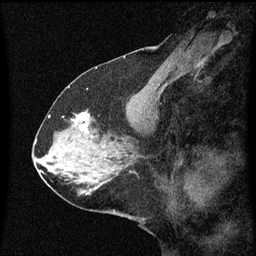
Breast MRI (dynamic contrast-enhanced), one sagittal slice. Slice 29 of 60 in the series (ordered by position). Dynamic contrast-enhanced series, image 2 of 3 at this slice position (ordered by acquisition). 1.5 T. TE 4.2 ms, TR 8.4 ms. 2 mm slice thickness. 256 × 256 image matrix, field of view 200 × 200 mm. Patient: female, 59 years.
Annotated regions visible in this slice (semi-automatic segmentation, software-assisted and operator-edited):
- analysis volume of interest (the breast-tissue region the enhancement analysis was run in; not a lesion): bounding box <70,110,99,137> (left, top, right, bottom; pixels)
- tumour enhancement mask (voxels above the 70 % enhancement threshold inside the analysis volume of interest): <74,112,91,133>